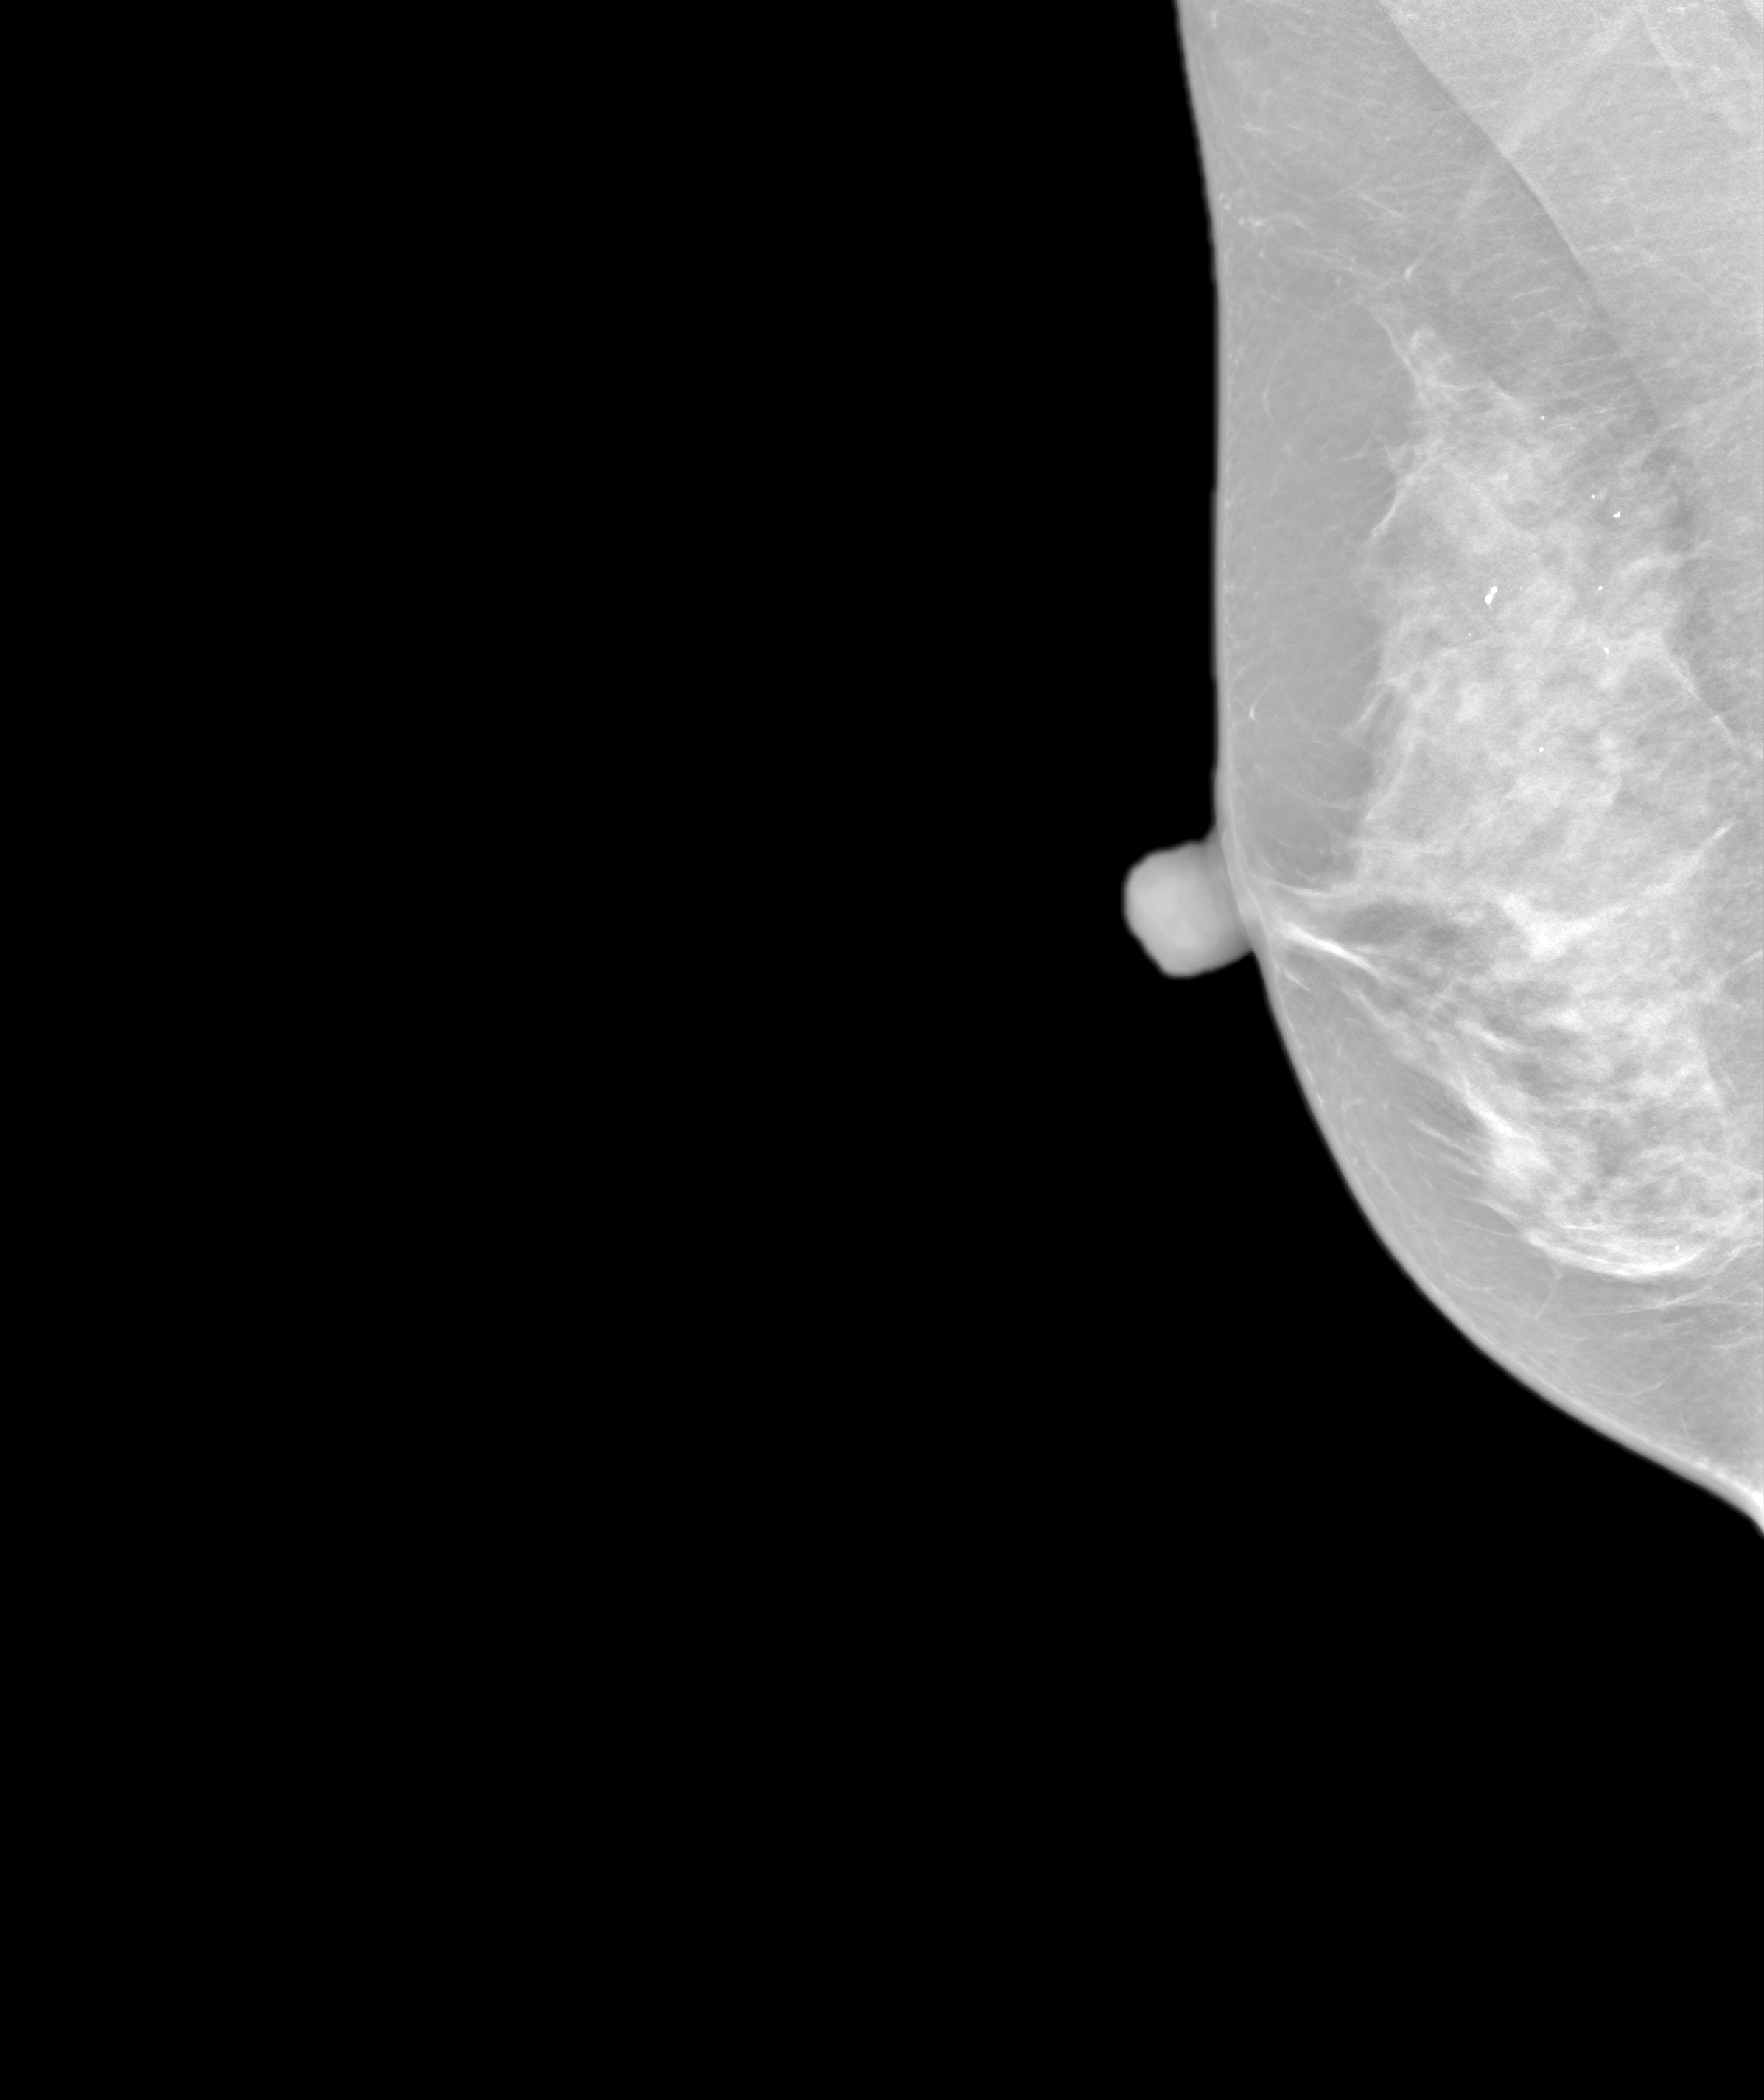
Annual screening mammography examination.
Image type: synthesized 2-D view from tomosynthesis. Breast: right. Projection: MLO view.